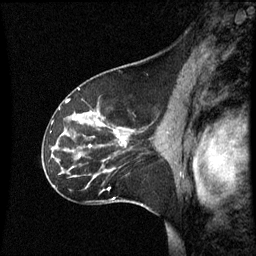
Breast MRI (dynamic contrast-enhanced), one sagittal slice. Slice 38 of 60 in the series (ordered by position). Dynamic contrast-enhanced series, image 2 of 3 at this slice position (ordered by acquisition). 1.5 T. TE 4.2 ms, TR 8.9 ms. 2 mm slice thickness. 256 × 256 image matrix. Patient: female, 45 years. From the clinical record (not read from this slice): setting: breast cancer imaged before/during neoadjuvant chemotherapy; receptor status: HR-positive, HER2-negative.
Annotated regions visible in this slice (semi-automatic segmentation, software-assisted and operator-edited):
- analysis volume of interest (the breast-tissue region the enhancement analysis was run in; not a lesion): bounding box <46,94,171,205> (left, top, right, bottom; pixels)
- tumour enhancement mask (voxels above the 70 % enhancement threshold inside the analysis volume of interest): <90,132,125,147>